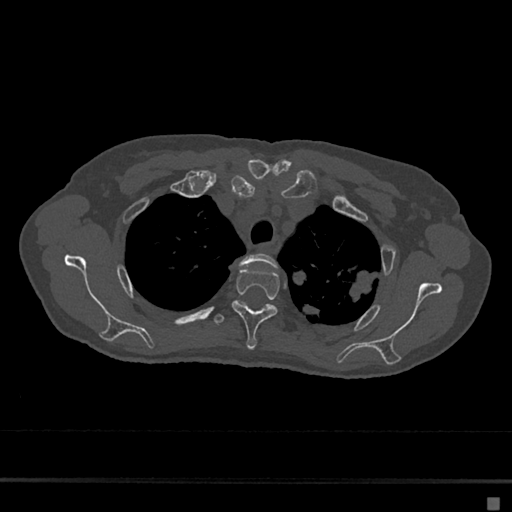
CT including the spine, one axial slice; position 536 of 797 along the scan axis; bone window (W 1800 / L 400 HU); 0.5 mm slice thickness; 512 × 512 image matrix. Patient: female, 68 years. From the clinical record (not read from this slice): primary cancer: renal.
Annotated regions visible in this slice (semi-automatically segmented with operator editing):
- T2 vertebra: bounding box <234,253,278,305> (left, top, right, bottom; pixels)
- T3 vertebra: <232,268,280,350>
- T4 vertebra: <214,305,272,325>